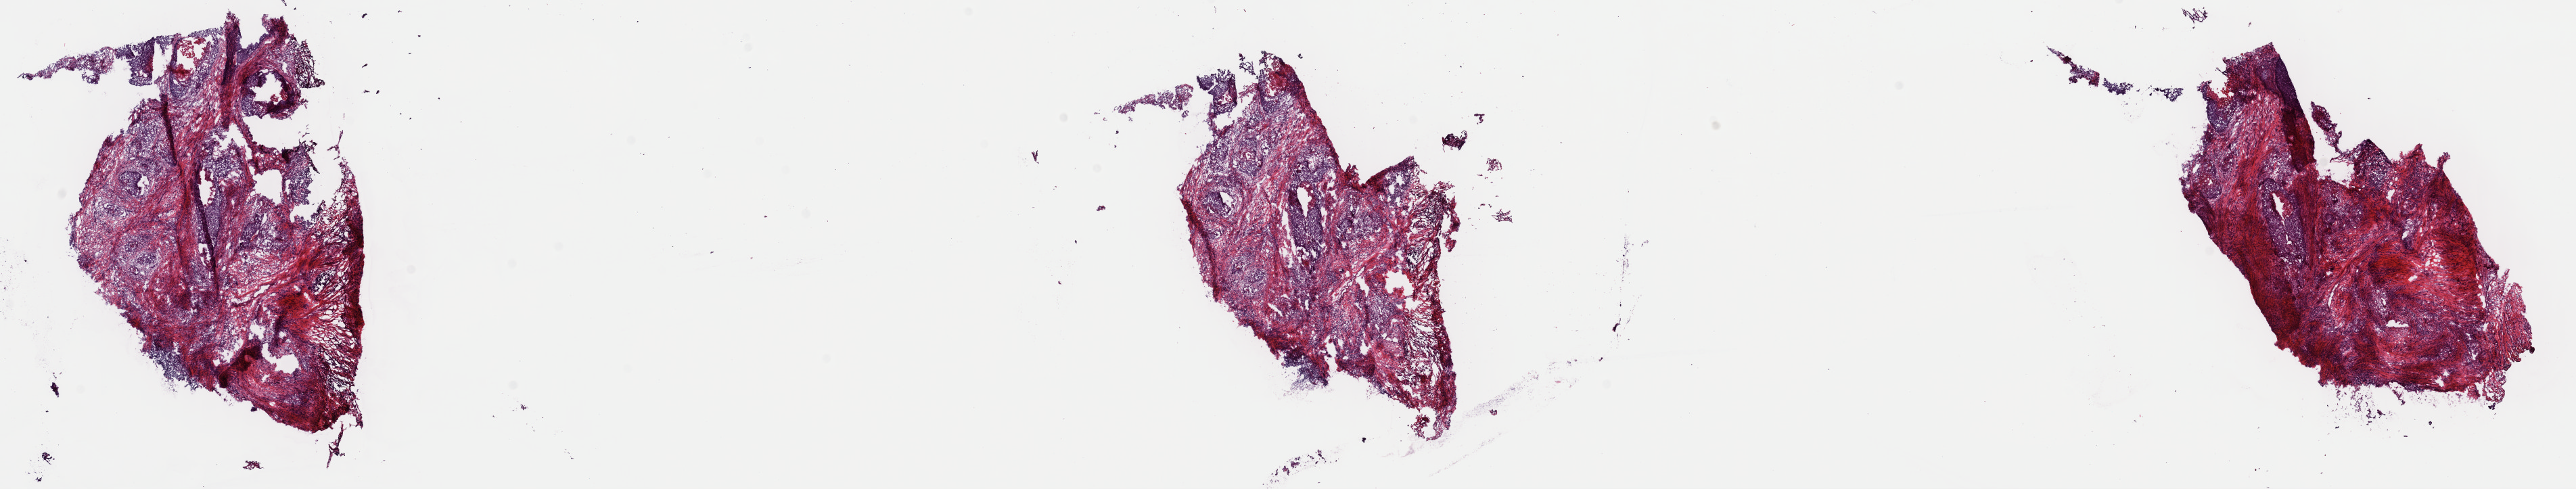
Digitized H&E tissue section (whole slide) — shown as a low-resolution overview of the whole scanned area (about 30.1 x 5.7 mm, from a 40x scan), frozen section from the top of the tissue portion, sample: primary tumour, head and neck. Male, age 76 years at initial diagnosis. Histologic grade: G2 (moderately differentiated). Slide review estimates, as recorded: tumour cells 45%, tumour nuclei 60%, normal cells 0%, stromal cells 52%, necrosis 3%. Inflammatory infiltration, as recorded: lymphocyte infiltration 10%, monocyte infiltration 6%, neutrophil infiltration 0%.
• AJCC pathologic stage: II (7th edition)
• TNM: T2 N0 MX
• pathologic diagnosis: Squamous cell carcinoma, keratinizing, NOS (tongue, NOS)